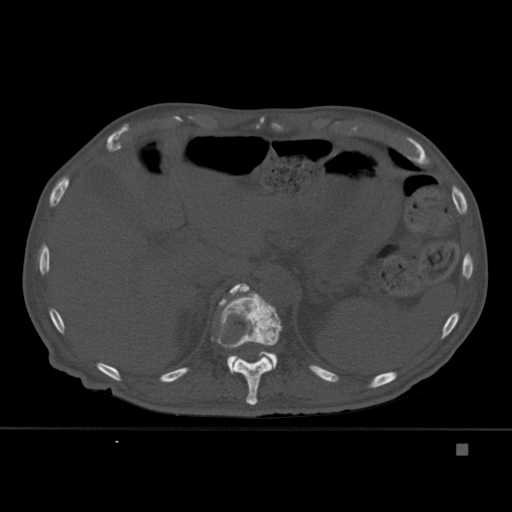
CT including the spine, one axial slice. Slice 213 of 451 in the series (ordered by position). Bone window (W 1800 / L 400 HU). 1.5 mm slice thickness. 512 × 512 image matrix. Patient: male, 75 years. From the clinical record (not read from this slice): primary cancer: prostate.
Annotated regions visible in this slice (semi-automatic segmentation, software-assisted and operator-edited):
- T11 vertebra: bounding box (x1, y1, x2, y2) in pixels: (211, 285, 282, 405)
- T12 vertebra: (221, 284, 277, 374)